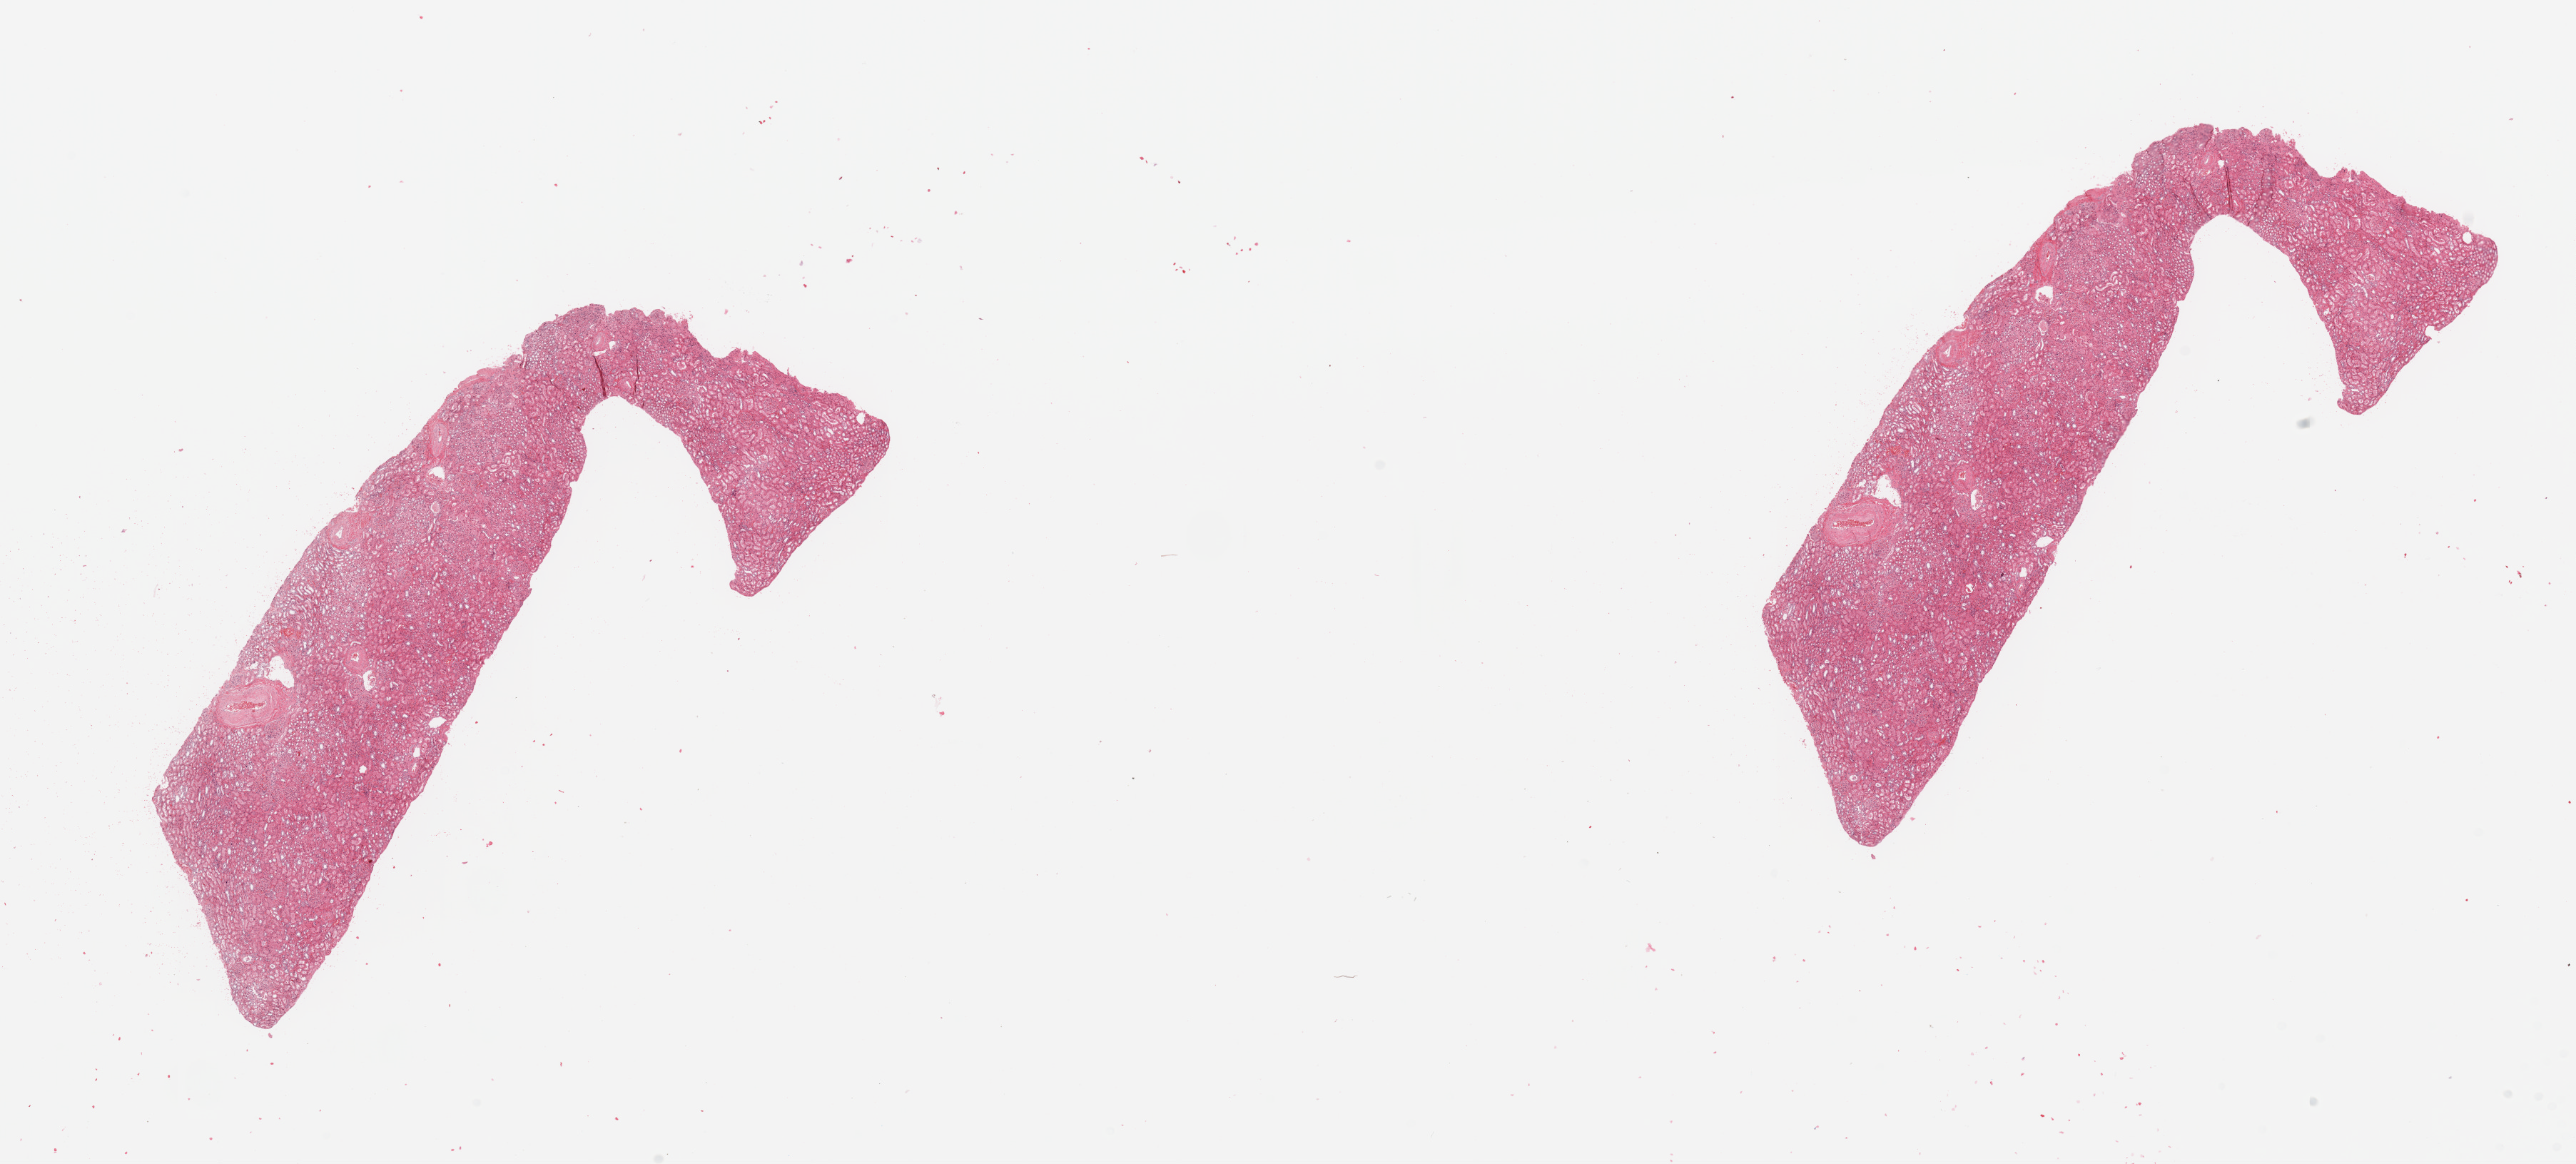
Digitized H&E tissue section (whole slide), shown as a low-resolution overview of the whole scanned area (about 28.5 x 12.9 mm); kidney, normal (non-tumour) tissue. Patient: male, age 41 years.
This section: normal (non-tumour) tissue from the same patient. Patient diagnosis: Renal cell carcinoma, NOS.